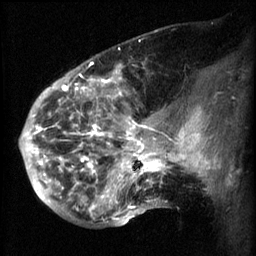
Breast MRI (dynamic contrast-enhanced), one sagittal slice; slice 22 of 60 in the series (ordered by position); 3 images stored at this slice position (order not interpretable as contrast timing); 1.5 T; TE 4.2 ms, TR 8.2 ms; 256 × 256 image matrix, field of view 200 × 200 mm. Patient: female, 50 years.
Outlined on this slice (semi-automatic segmentation, software-assisted and operator-edited):
- analysis volume of interest (the breast-tissue region the enhancement analysis was run in; not a lesion): bounding box [x1, y1, x2, y2] px = [50, 64, 169, 217]
- tumour enhancement mask (voxels above the 70 % enhancement threshold inside the analysis volume of interest): [50, 64, 167, 215]